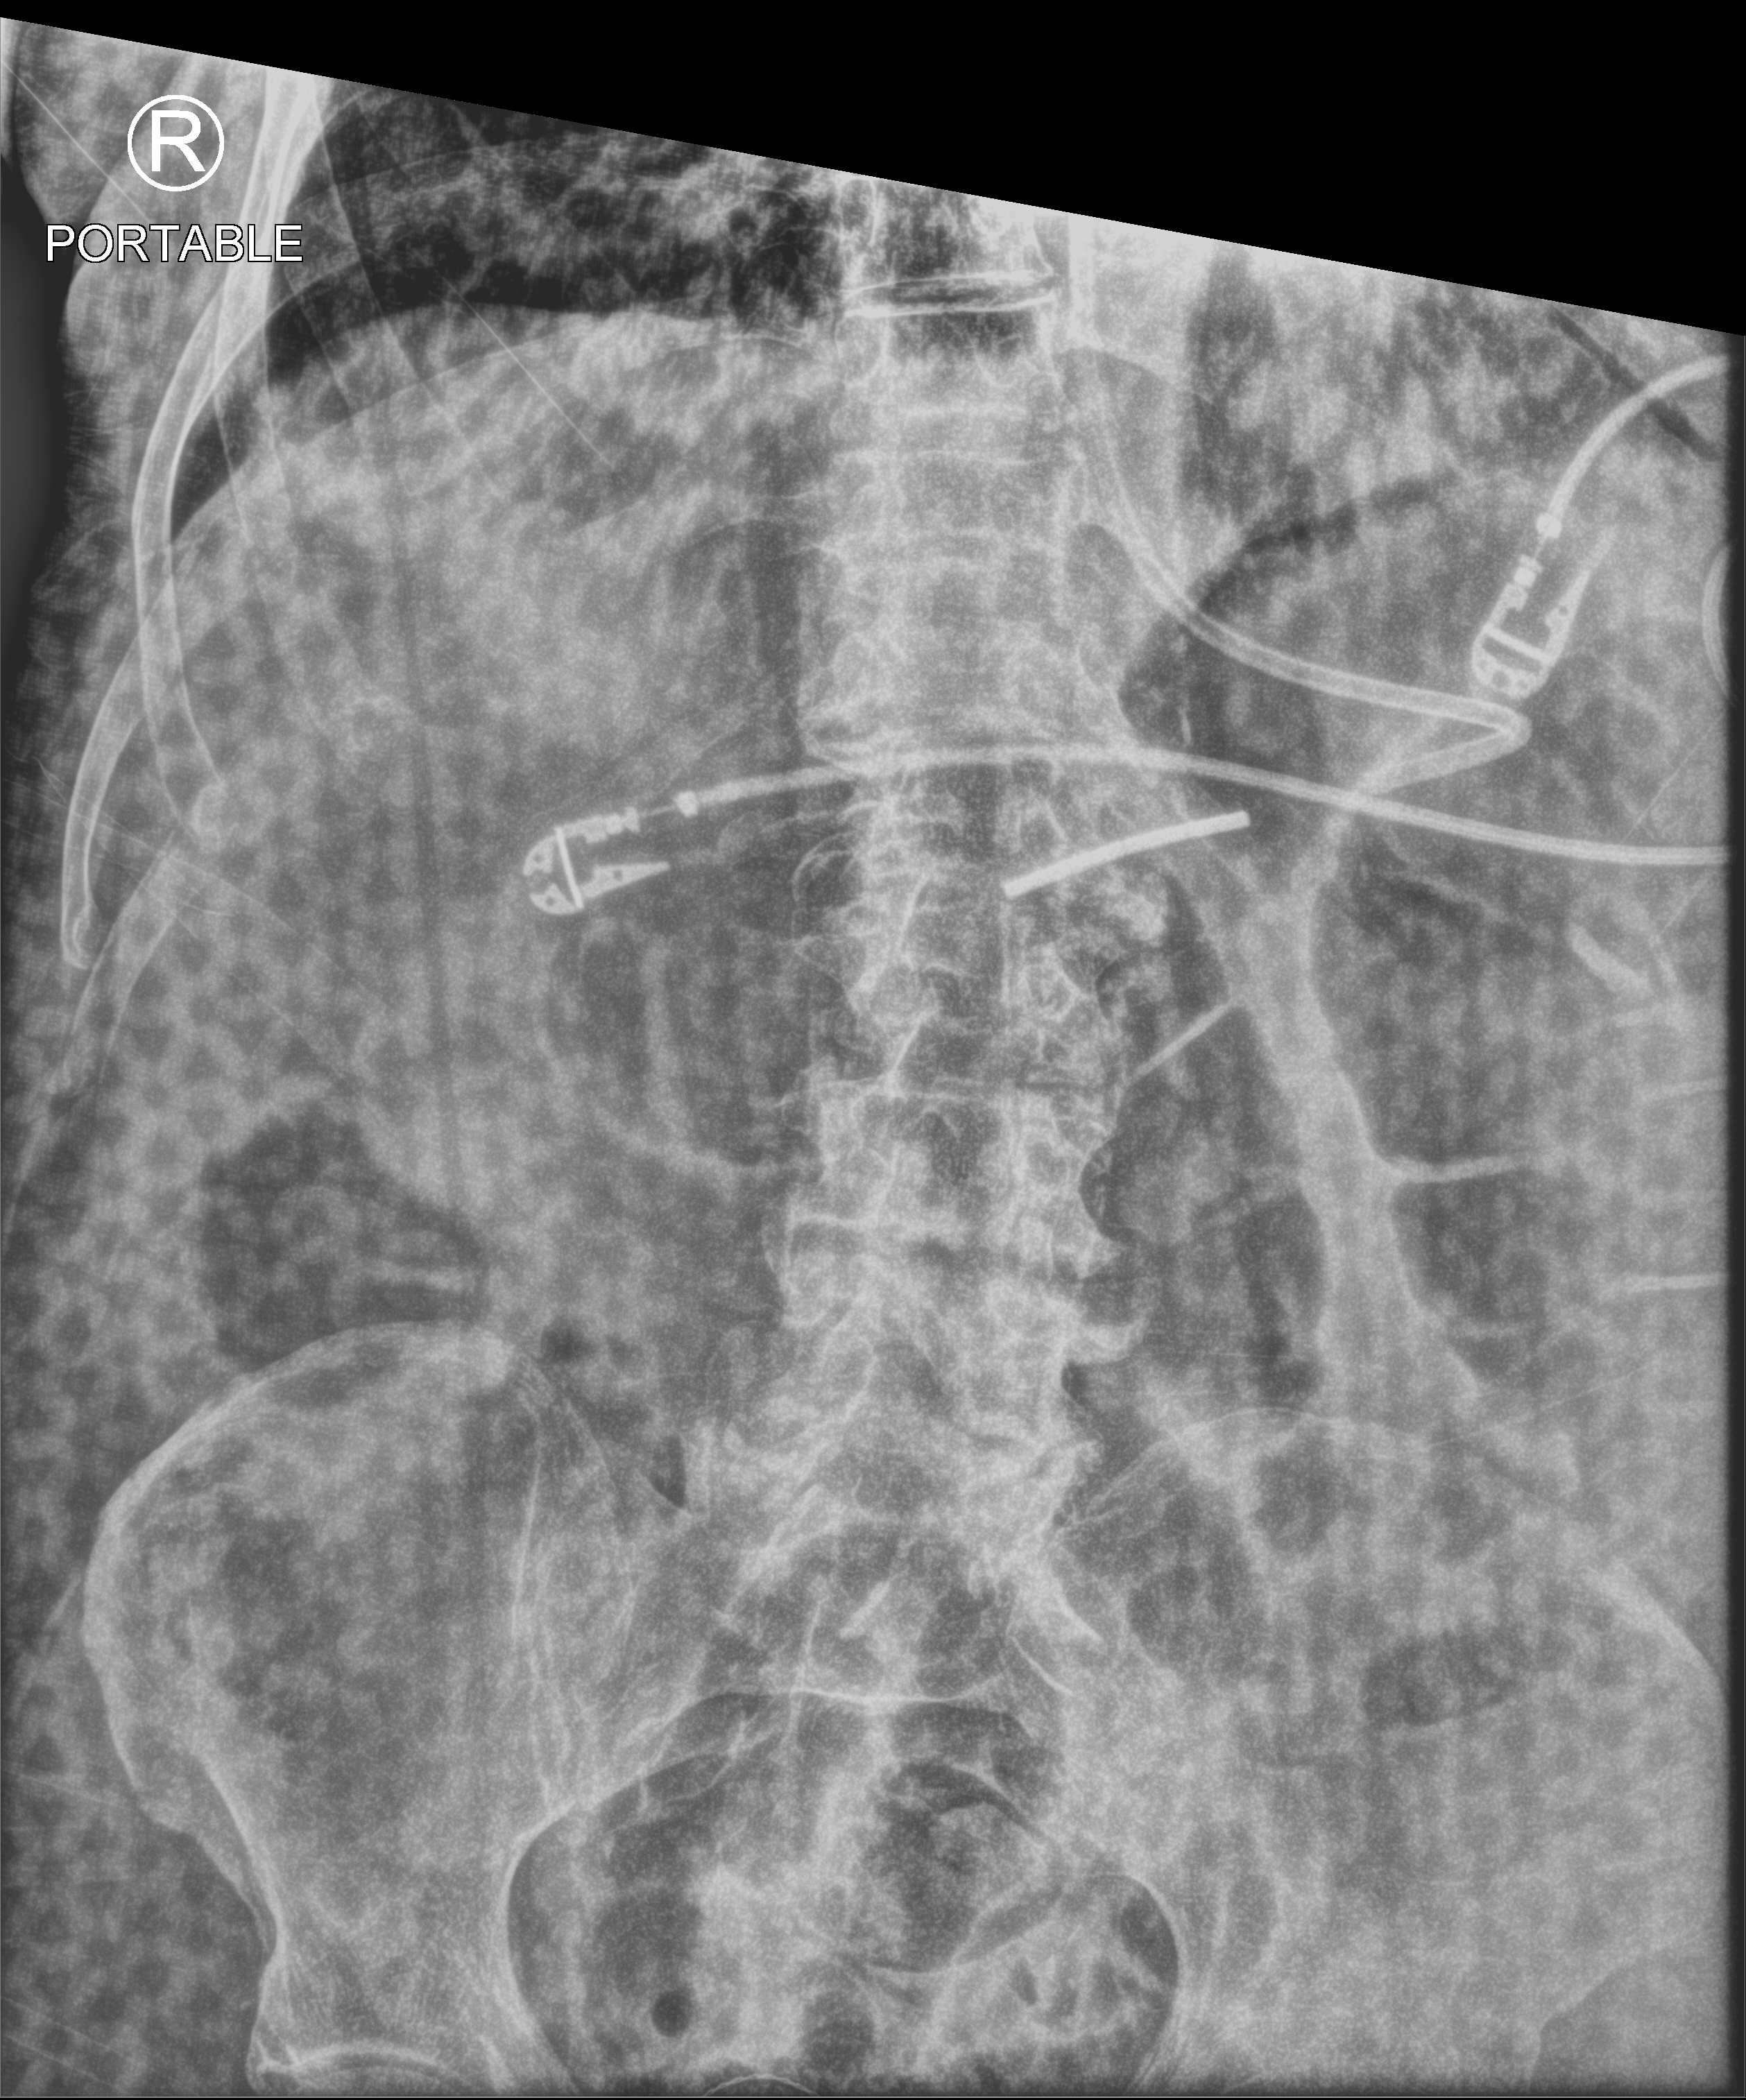
Portable abdomen radiograph, anteroposterior (AP) projection. Patient hospitalised with COVID-19; male, aged 75–90 years.
Hospital-stay facts (about this admission, not read from this image; timing relative to this image not recorded): COPD (admission record): no.